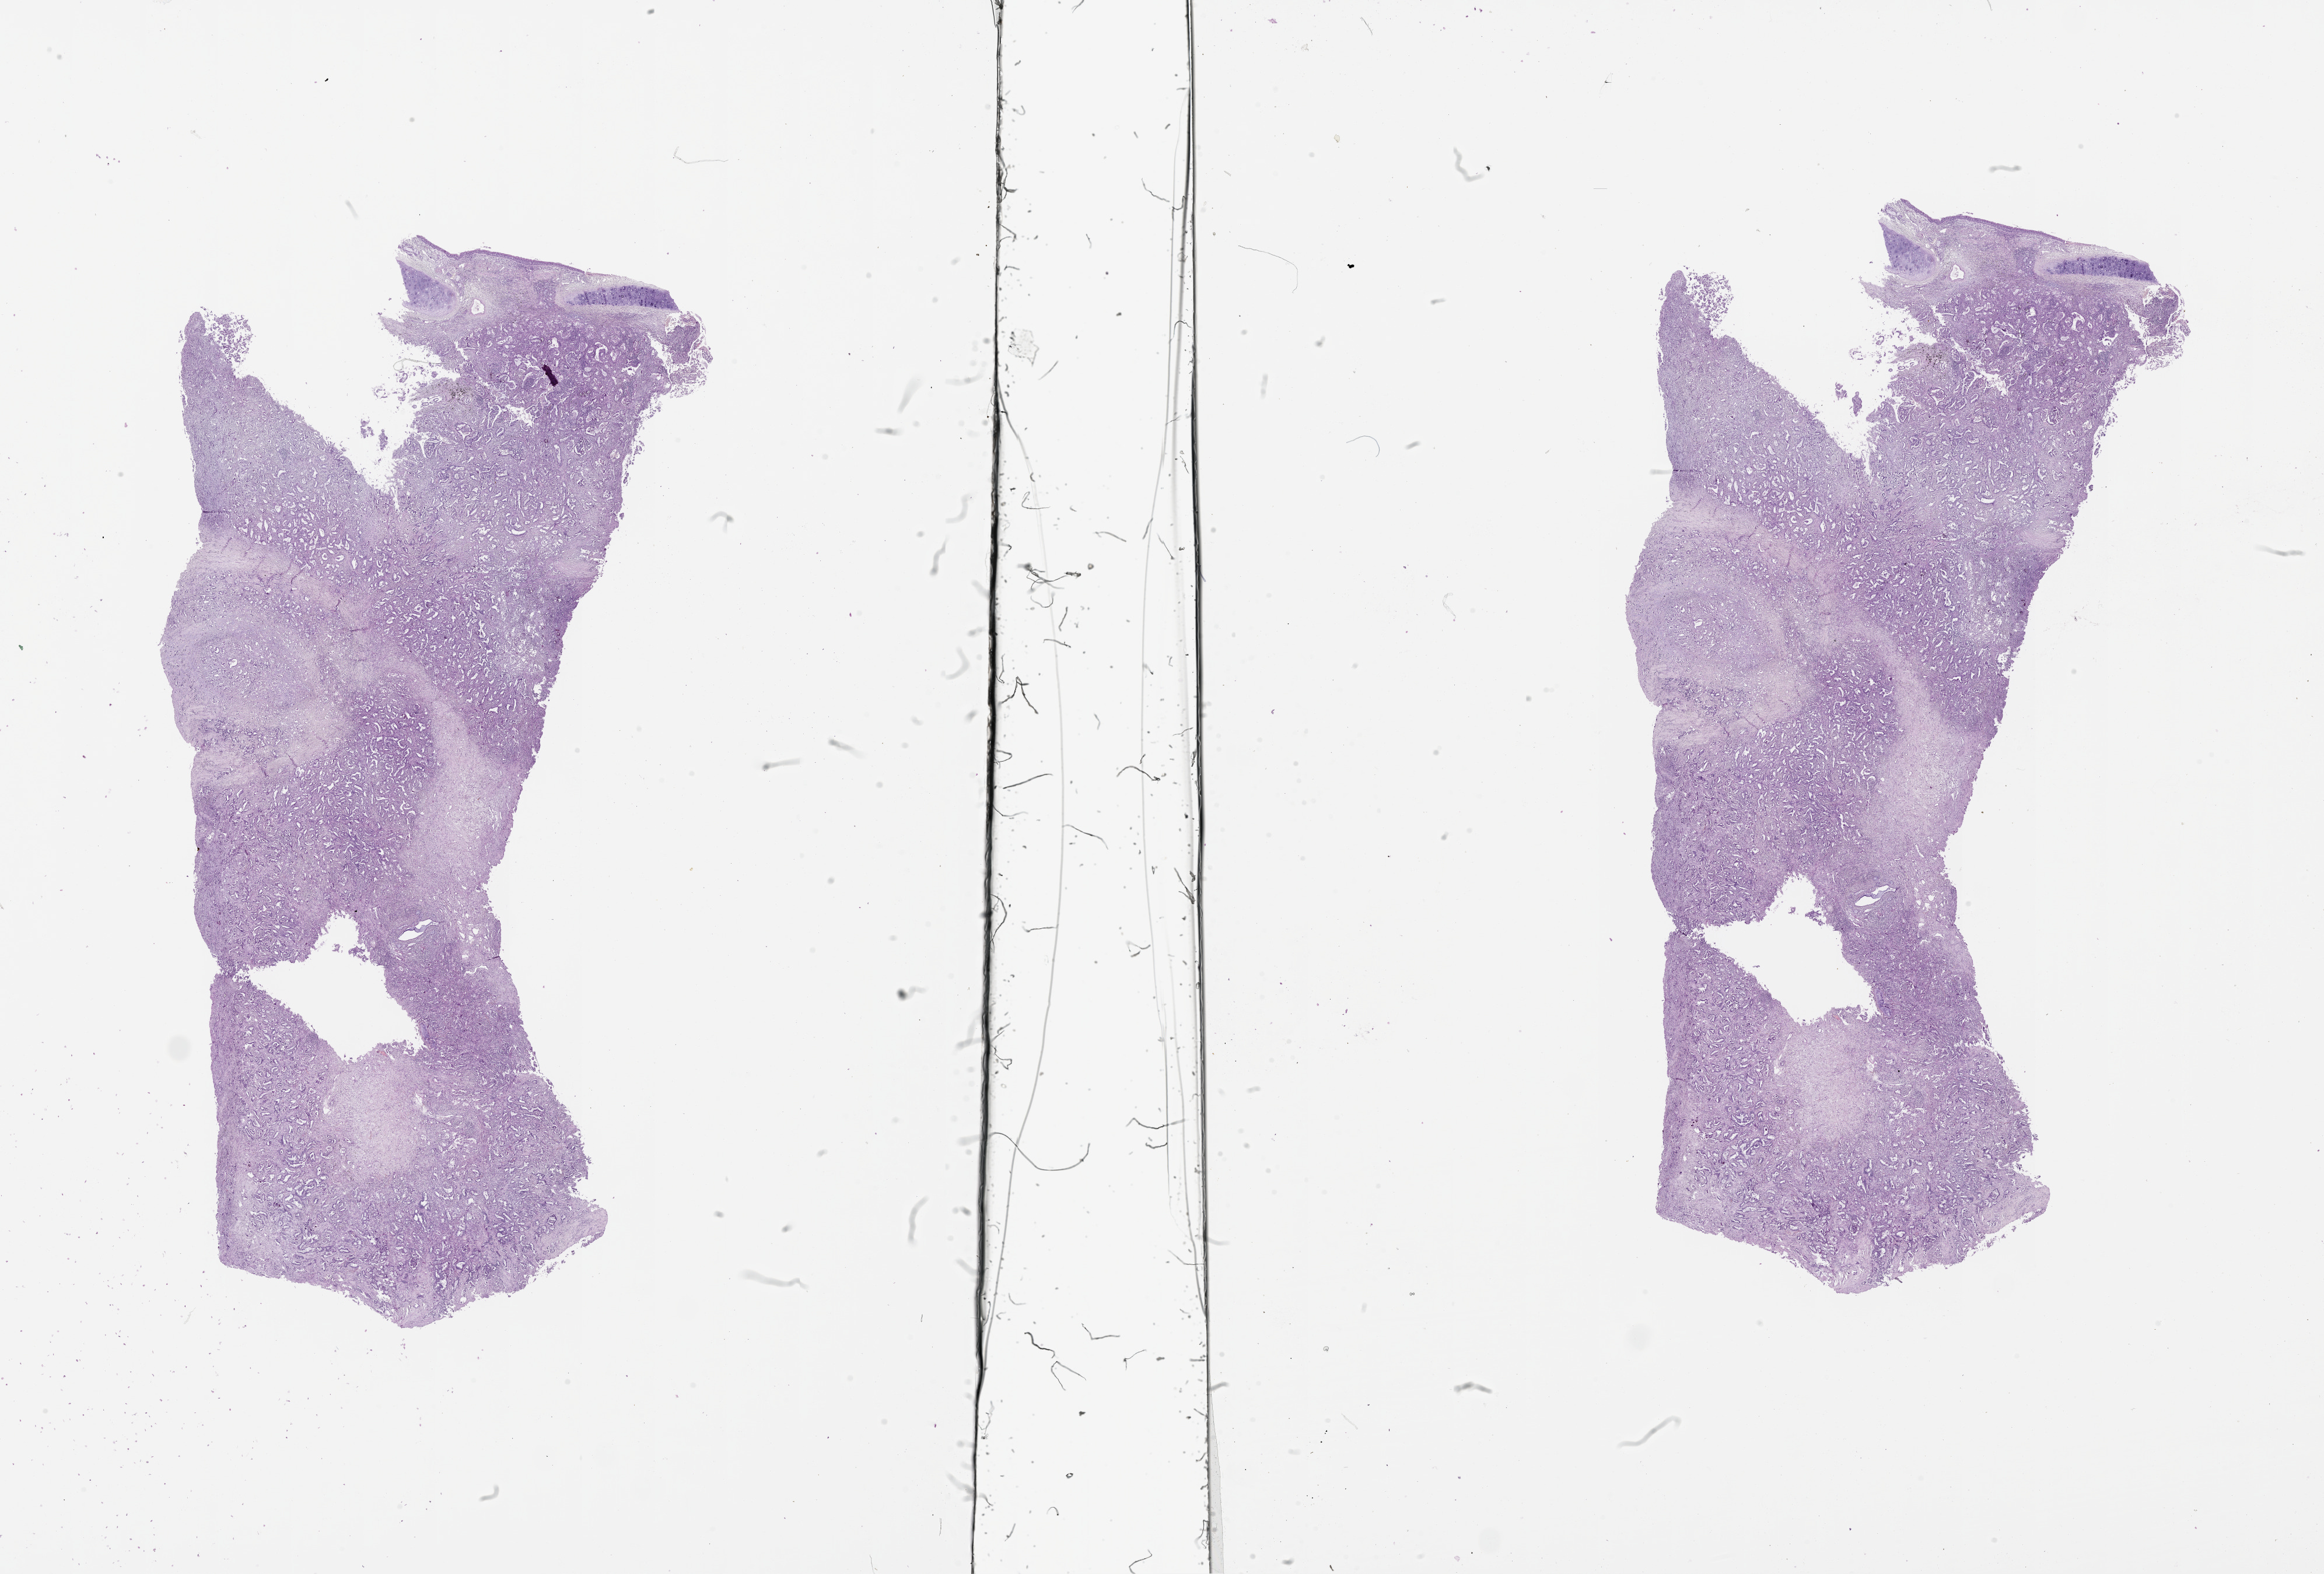
Whole-slide histology image, Hematoxylin and eosin (H&E) stained — a low-resolution overview of the entire scanned area, about 32.1 x 21.7 mm (slide scanned at 20x). Tumour tissue sample, sampled site: lung. Patient: male, age 61 years. Histologic grade: G2 (moderately differentiated). Slide review estimates, as recorded: tumour nuclei 75%, necrosis 5%.
Primary tumour site (as recorded): right upper lobe. AJCC pathologic stage: IIIA. Histologic diagnosis: Adenocarcinoma, NOS.